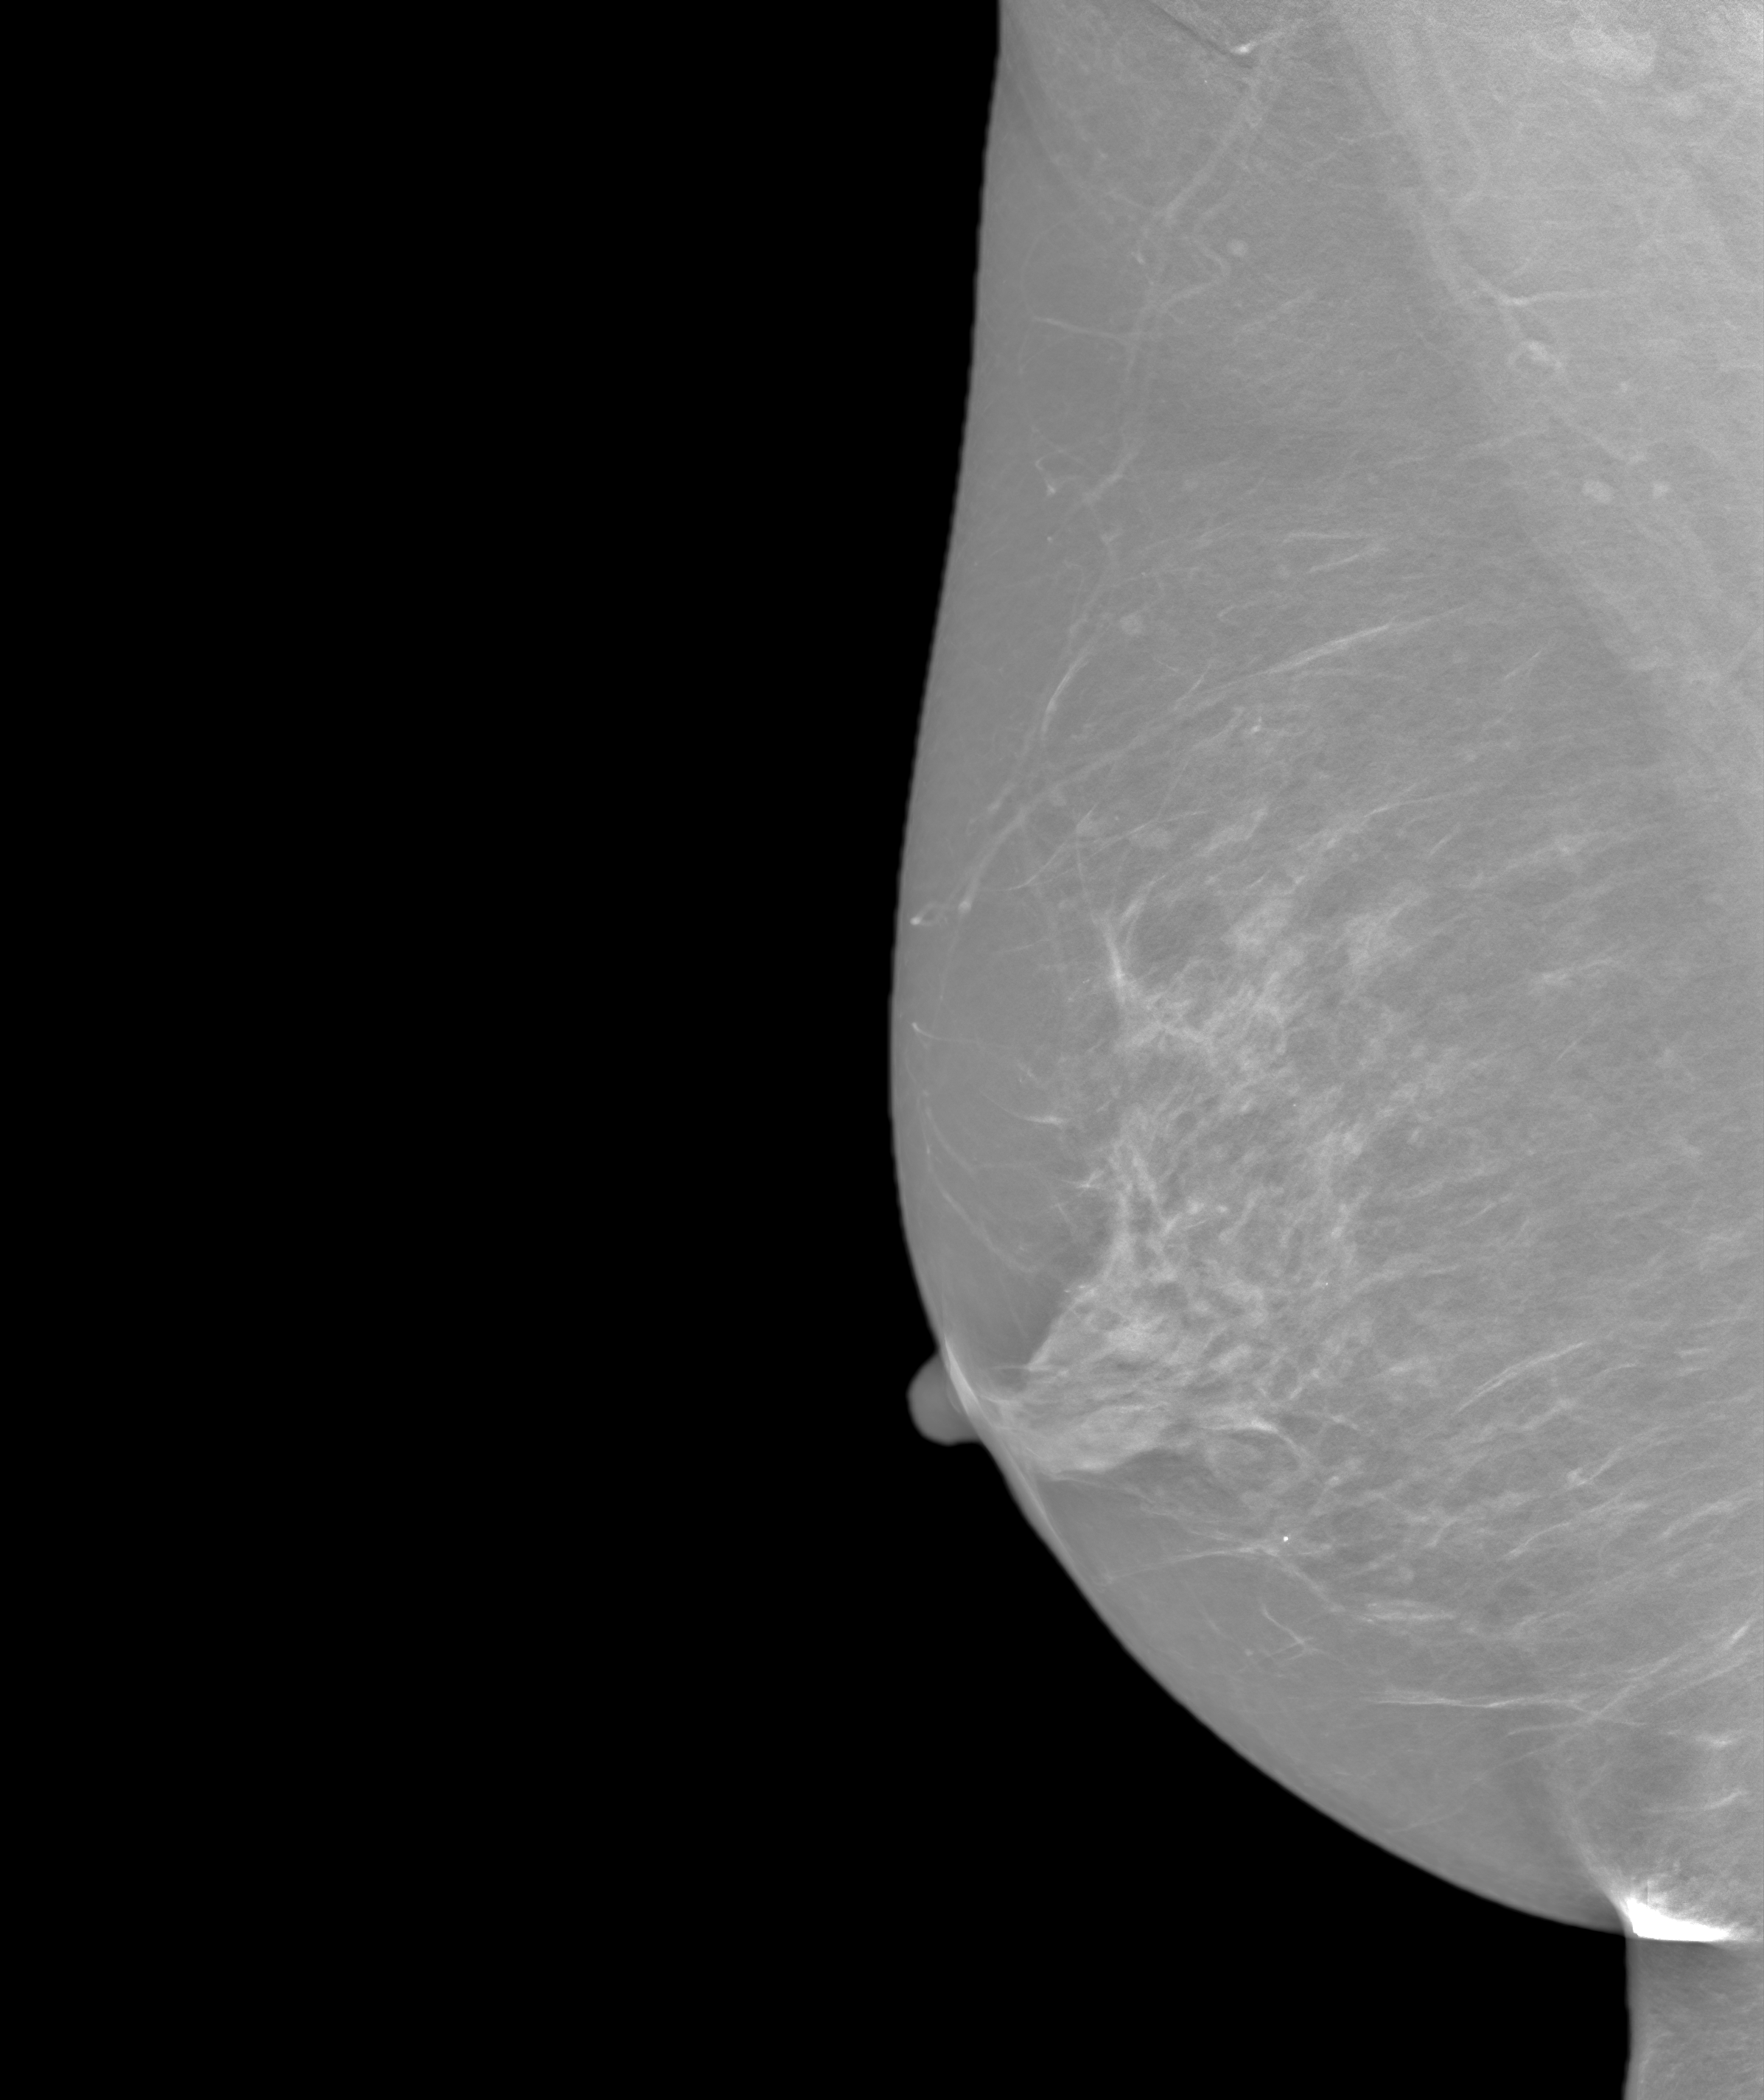
Annual screening mammography examination. Patient: female, 54 years.
Image type: synthesized 2-D view from tomosynthesis. Breast: right. Projection: medio-lateral oblique projection.